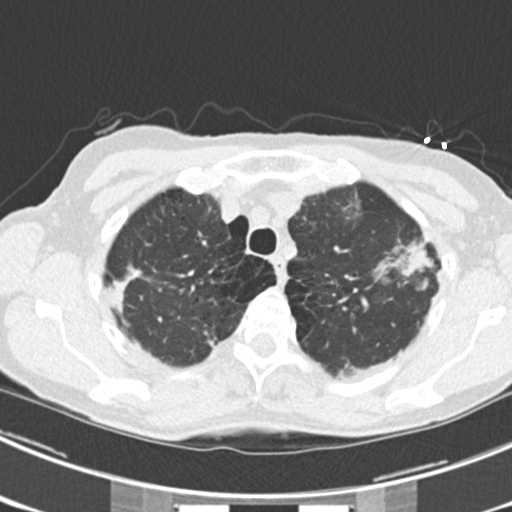
Axial slice from a low-dose chest CT screening exam, third screening round (two years after baseline), lung window (W 1500 / L -600 HU), standard (soft-tissue) reconstruction kernel (B30f), slice 46 of 225 in the series, 512 × 512 image matrix, field of view 302 × 302 mm. Female, age 63 years at enrolment. Current smoker at enrolment.
Expert-annotated lung lesion, box from (x=375, y=230) to (x=445, y=292) px. The screening reader recorded 9 non-calcified nodules or masses ≥4 mm on this exam; which of them this box marks is not recorded.